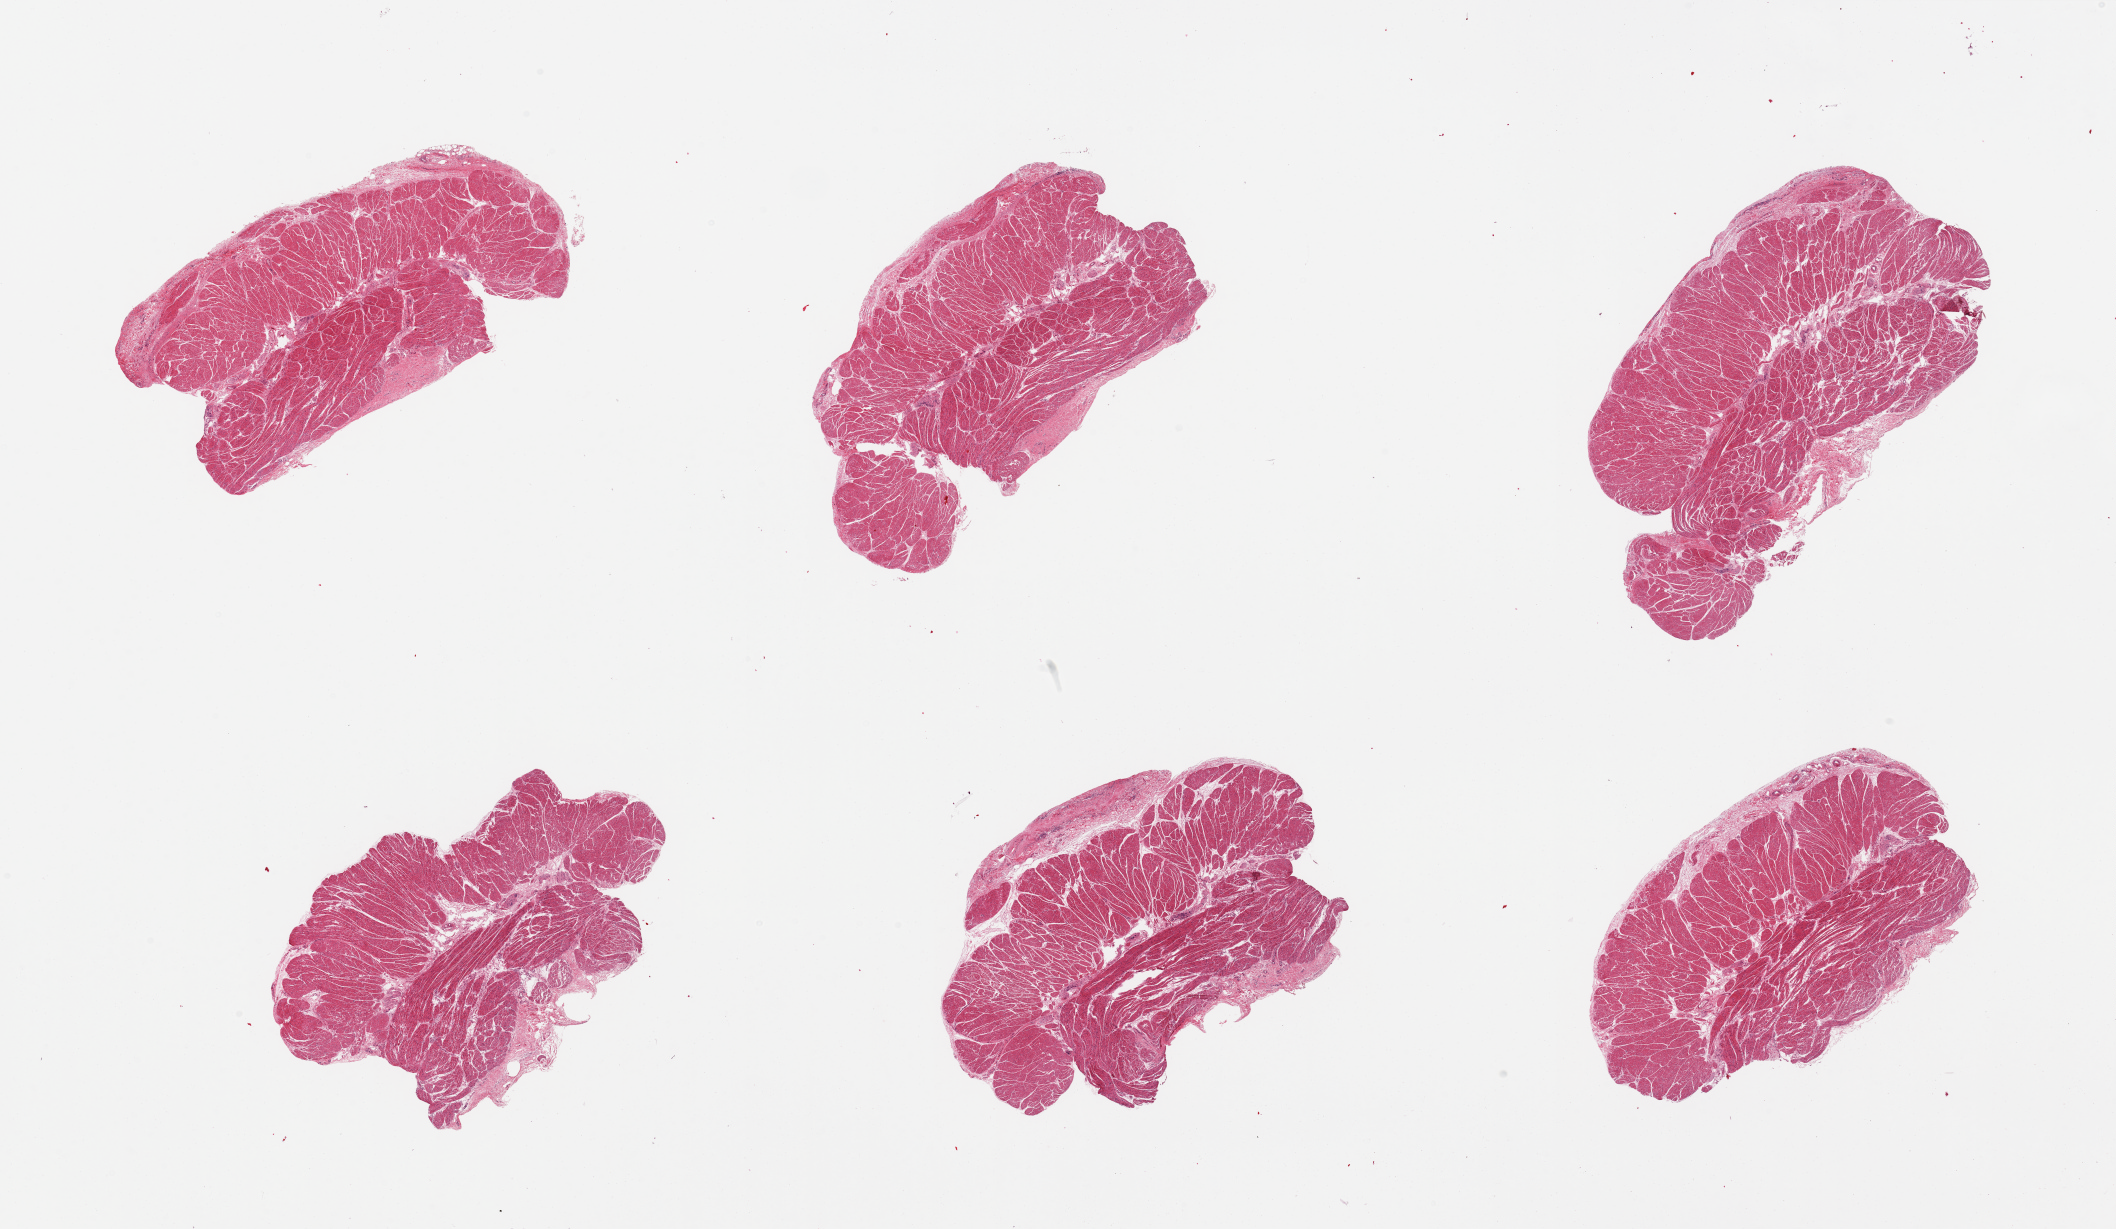
Whole-slide image, haematoxylin and eosin stain, whole scanned area (about 33.5 x 19.4 mm, acquisition: 20x scan) shown as a low-resolution overview; PAXgene-fixed paraffin-embedded (PFPE) section; target tissue: esophageal muscle; donor tissue sample. Female donor.
Review note (as recorded): 6 pieces, all muscularis, good specimens.